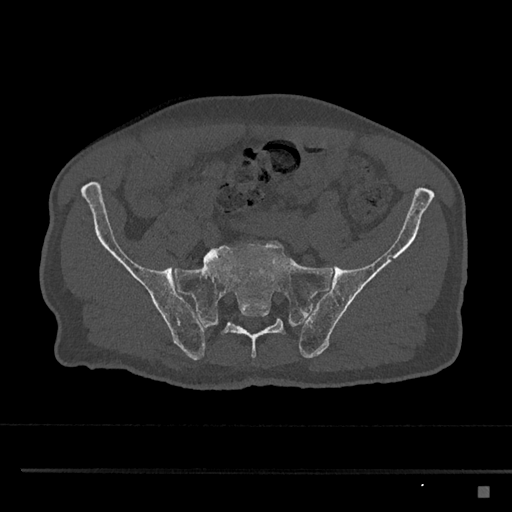
CT including the spine, one axial slice; slice 516 of 797 in the series (ordered by position); reconstruction kernel Br40s/3; bone window (W 1800 / L 400 HU); 512 × 512 image matrix. Patient: male, 59 years. Case-level facts recorded for this patient, not image findings: primary cancer: prostate.
Outlined on this slice (semi-automatically segmented with operator editing):
- L5 vertebra: box from (x=204, y=254) to (x=210, y=259) px